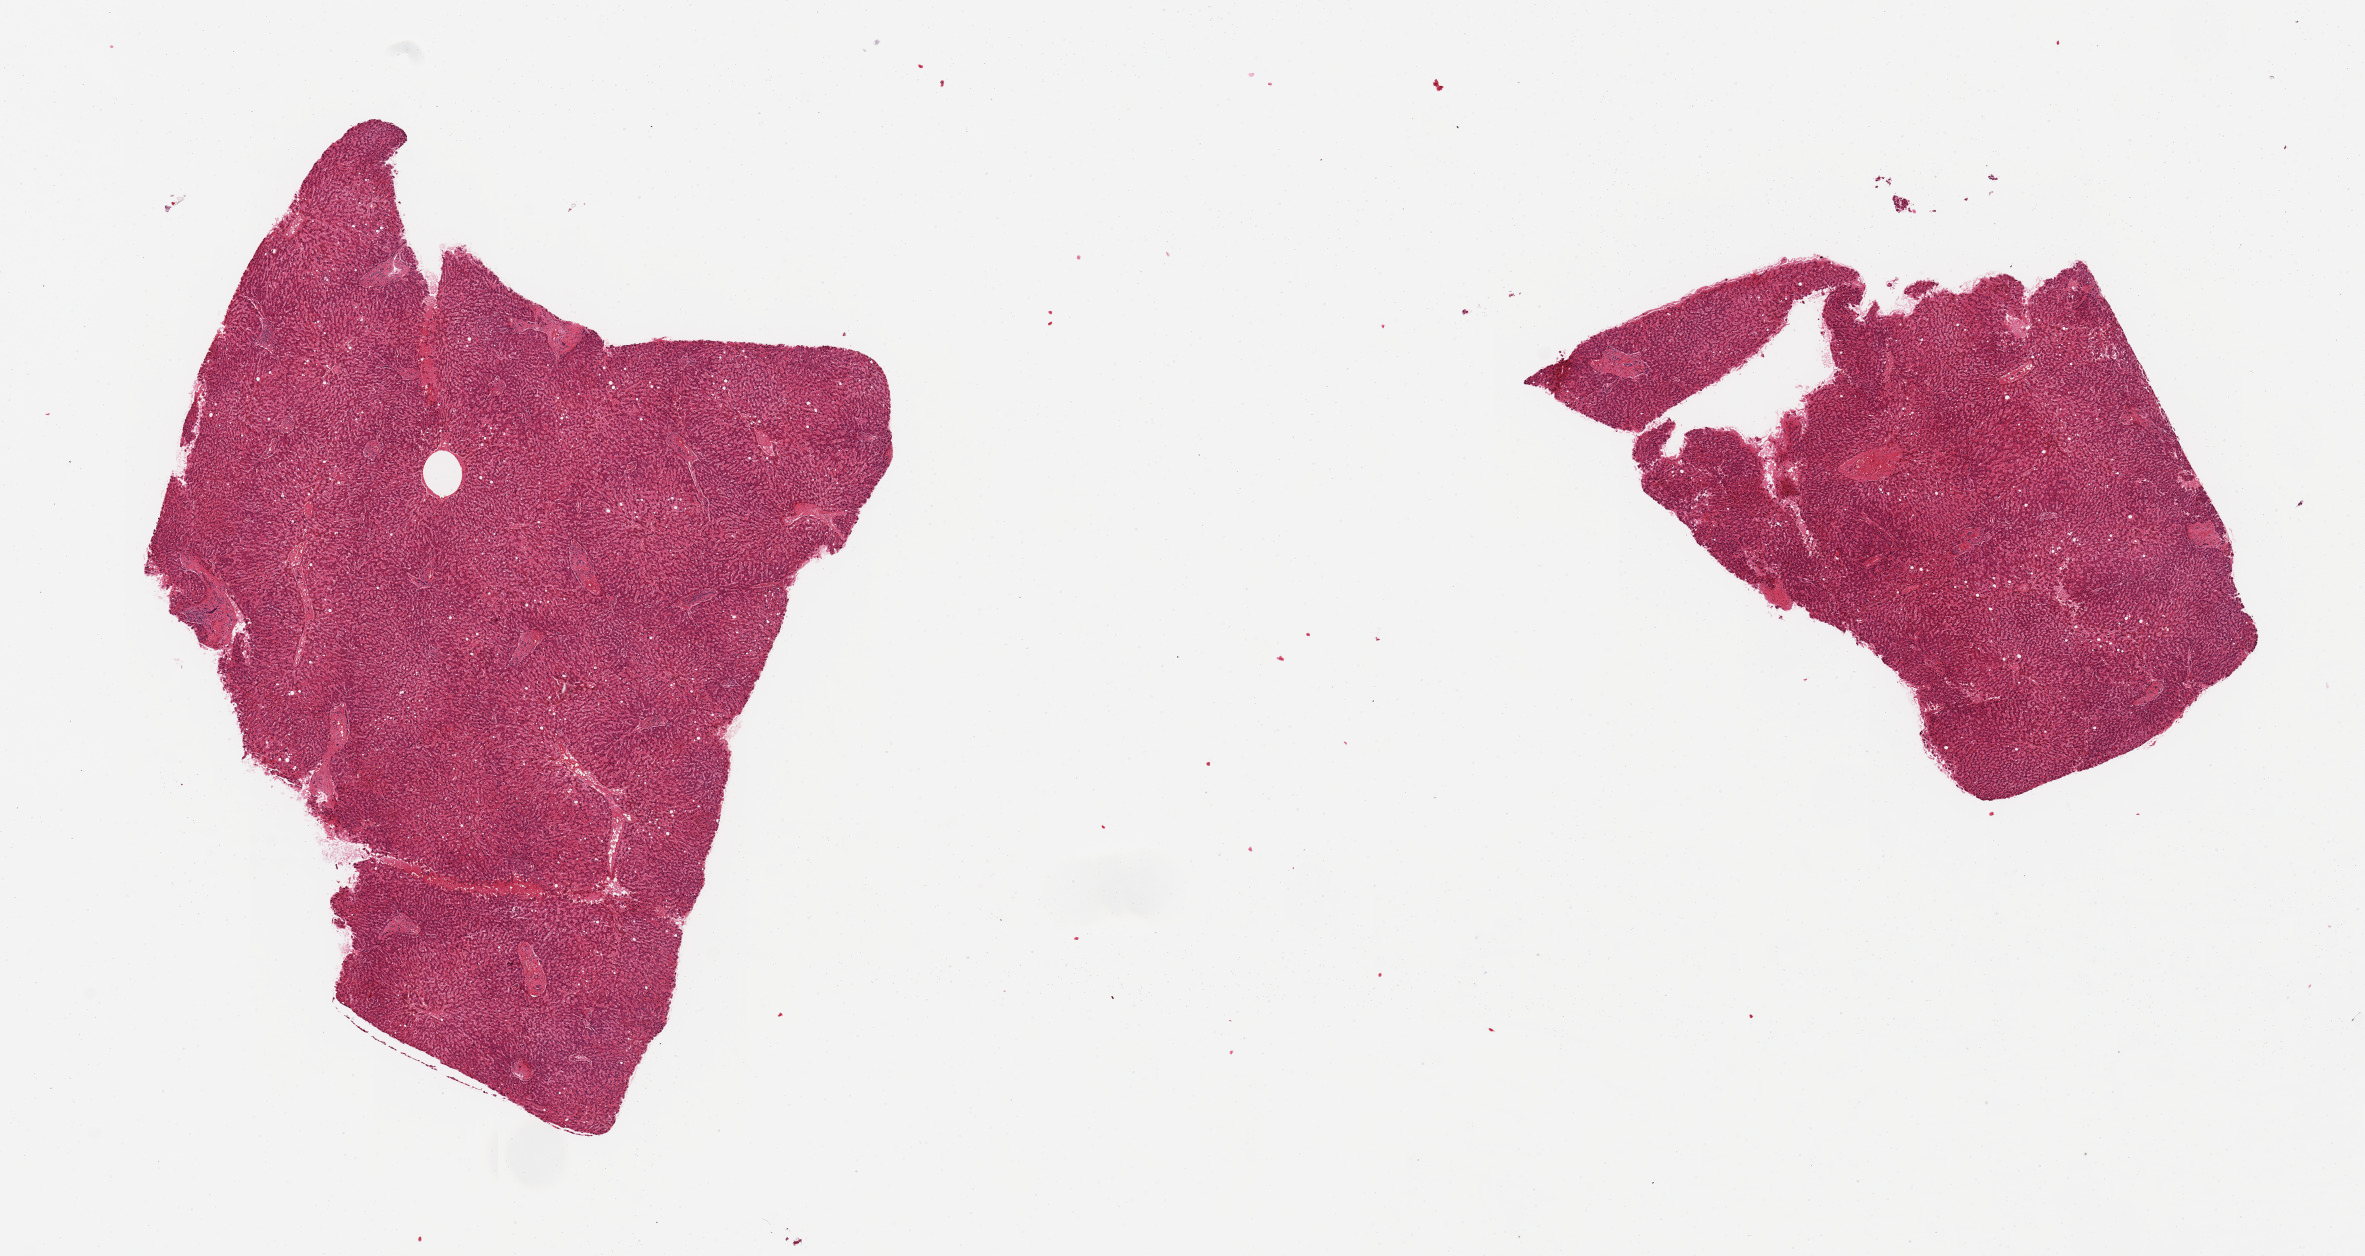
Whole-slide image, hematoxylin and eosin (H&E) stain — low-resolution overview of the scanned area, about 18.7 x 9.9 mm, PAXgene-fixed paraffin-embedded (PFPE) section, sampled site (target tissue): liver, donor tissue sample. Donor sex: male.
Pathologist's review note for this sample: 2 pieces, ~ 5% macrovesicular fat.